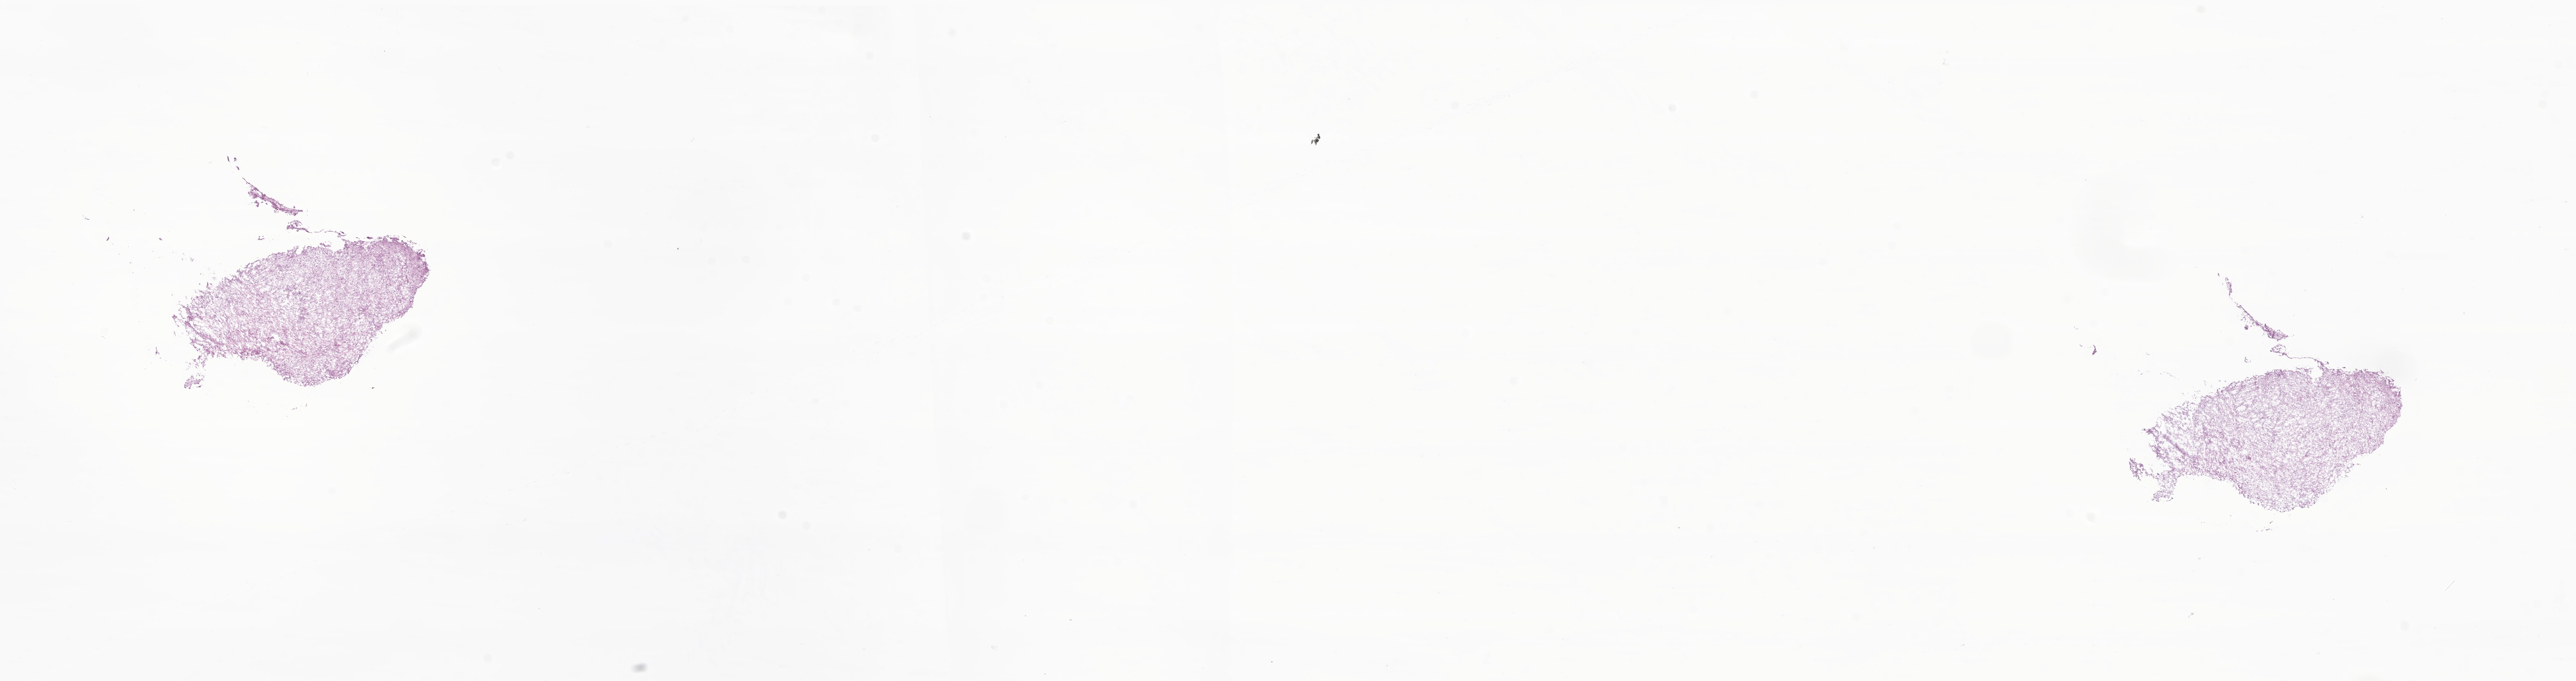
Whole-slide image, haematoxylin and eosin stain of tumor tissue from the cerebellum, low-resolution overview of the scanned area, about 28.9 x 7.6 mm, frozen section. Patient: female, age 41 months (3 years 5 months).
Diagnosis (ICD-O-3 morphology term): Pilocytic astrocytoma.